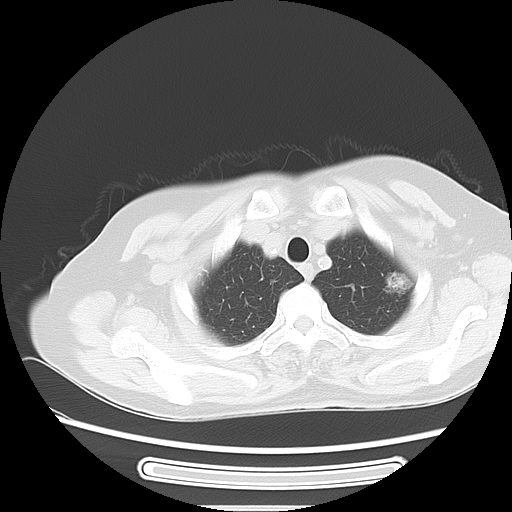
Chest CT, one axial slice; 120 kVp; lung window (W 1500 / L -600 HU); 5 mm slice thickness; 512 × 512 image matrix, field of view 350 × 350 mm. Patient: female, 57 years. Case-level facts recorded for this patient, not image findings: clinical TNM (as recorded): T1c N0 M0.
Structures marked on this image (rectangle marked by the reading radiologist):
- lung tumour (recorded histology: adenocarcinoma): box from (x=380, y=268) to (x=419, y=304) px